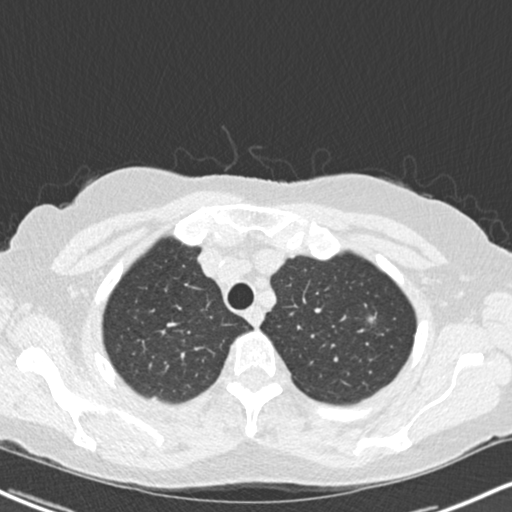
Axial slice from a low-dose chest CT screening exam, first (baseline) screen, lung window (W 1500 / L -600 HU), slice 28 of 217 in the series, 512 × 512 image matrix, field of view 319 × 319 mm. Female participant, aged 64 years at enrolment. Former smoker at enrolment.
Expert-annotated lung lesion, bounding box (x1, y1, x2, y2) in pixels: (358, 307, 392, 338). The screening reader recorded 2 non-calcified nodules or masses ≥4 mm on this exam; which of them this box marks is not recorded. Official screen result: positive, change unspecified: nodule(s) >= 4 mm or enlarging nodule(s), mass(es), or other non-specific abnormalities suspicious for lung cancer.